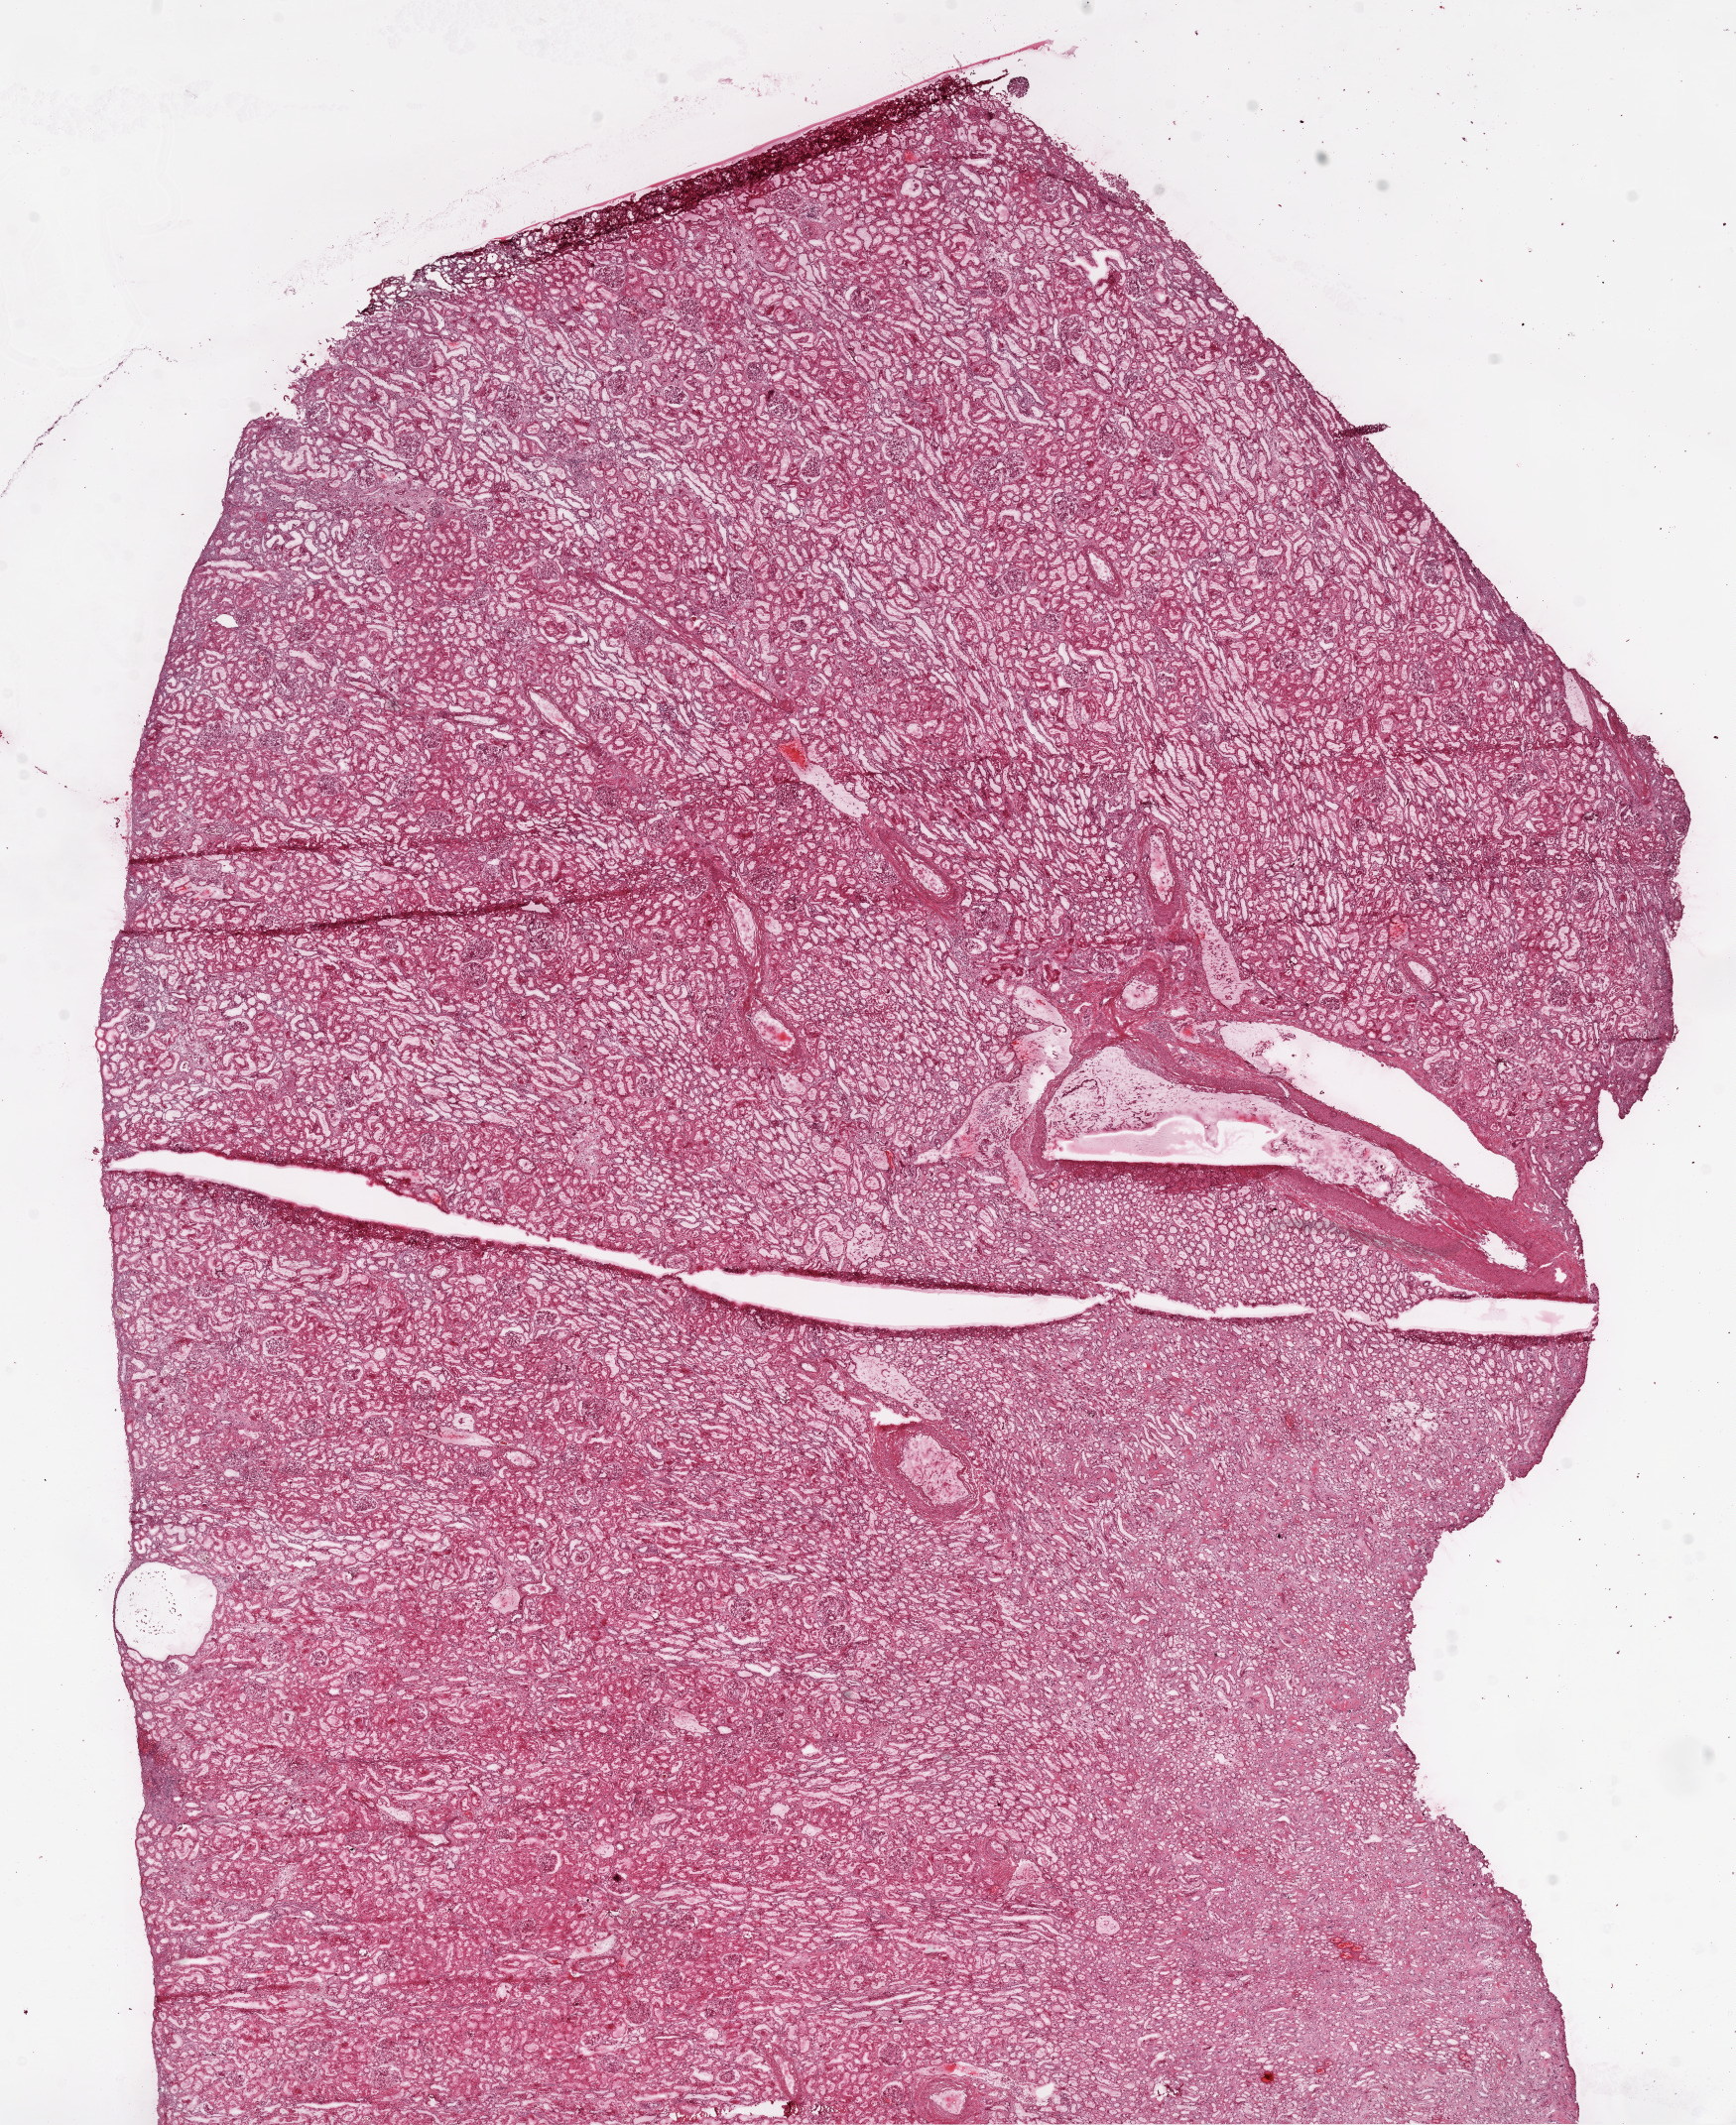
Whole-slide histology image, H&E, a low-resolution overview of the entire scanned area, about 14.0 x 17.2 mm, frozen section from the top of the tissue portion, solid tissue normal (non-tumour tissue) sample from the kidney. Patient: male, age at initial diagnosis 56 years.
This section: solid tissue normal (non-tumour) sample from the same patient. Patient diagnosis: Clear cell adenocarcinoma, NOS.